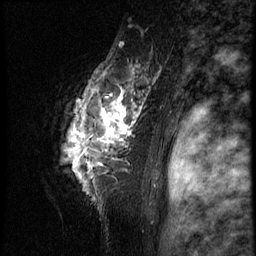
Breast MRI (dynamic contrast-enhanced), one sagittal slice; position 56 of 66 along the scan axis; 3 images stored at this slice position (order not interpretable as contrast timing); 1.5 T; TE 4.2 ms, TR 8.9 ms; 2.5 mm slice thickness; 256 × 256 image matrix. Female patient, age 39 years. Case-level facts recorded for this patient, not image findings: setting: breast cancer imaged before/during neoadjuvant chemotherapy; receptor status: HER2-positive.
Outlined on this slice (semi-automatic segmentation, software-assisted and operator-edited):
- analysis volume of interest (the breast-tissue region the enhancement analysis was run in; not a lesion): box from (x=46, y=44) to (x=166, y=196) px
- tumour enhancement mask (voxels above the 140 % enhancement threshold inside the analysis volume of interest): (x=67, y=82)–(x=144, y=163)